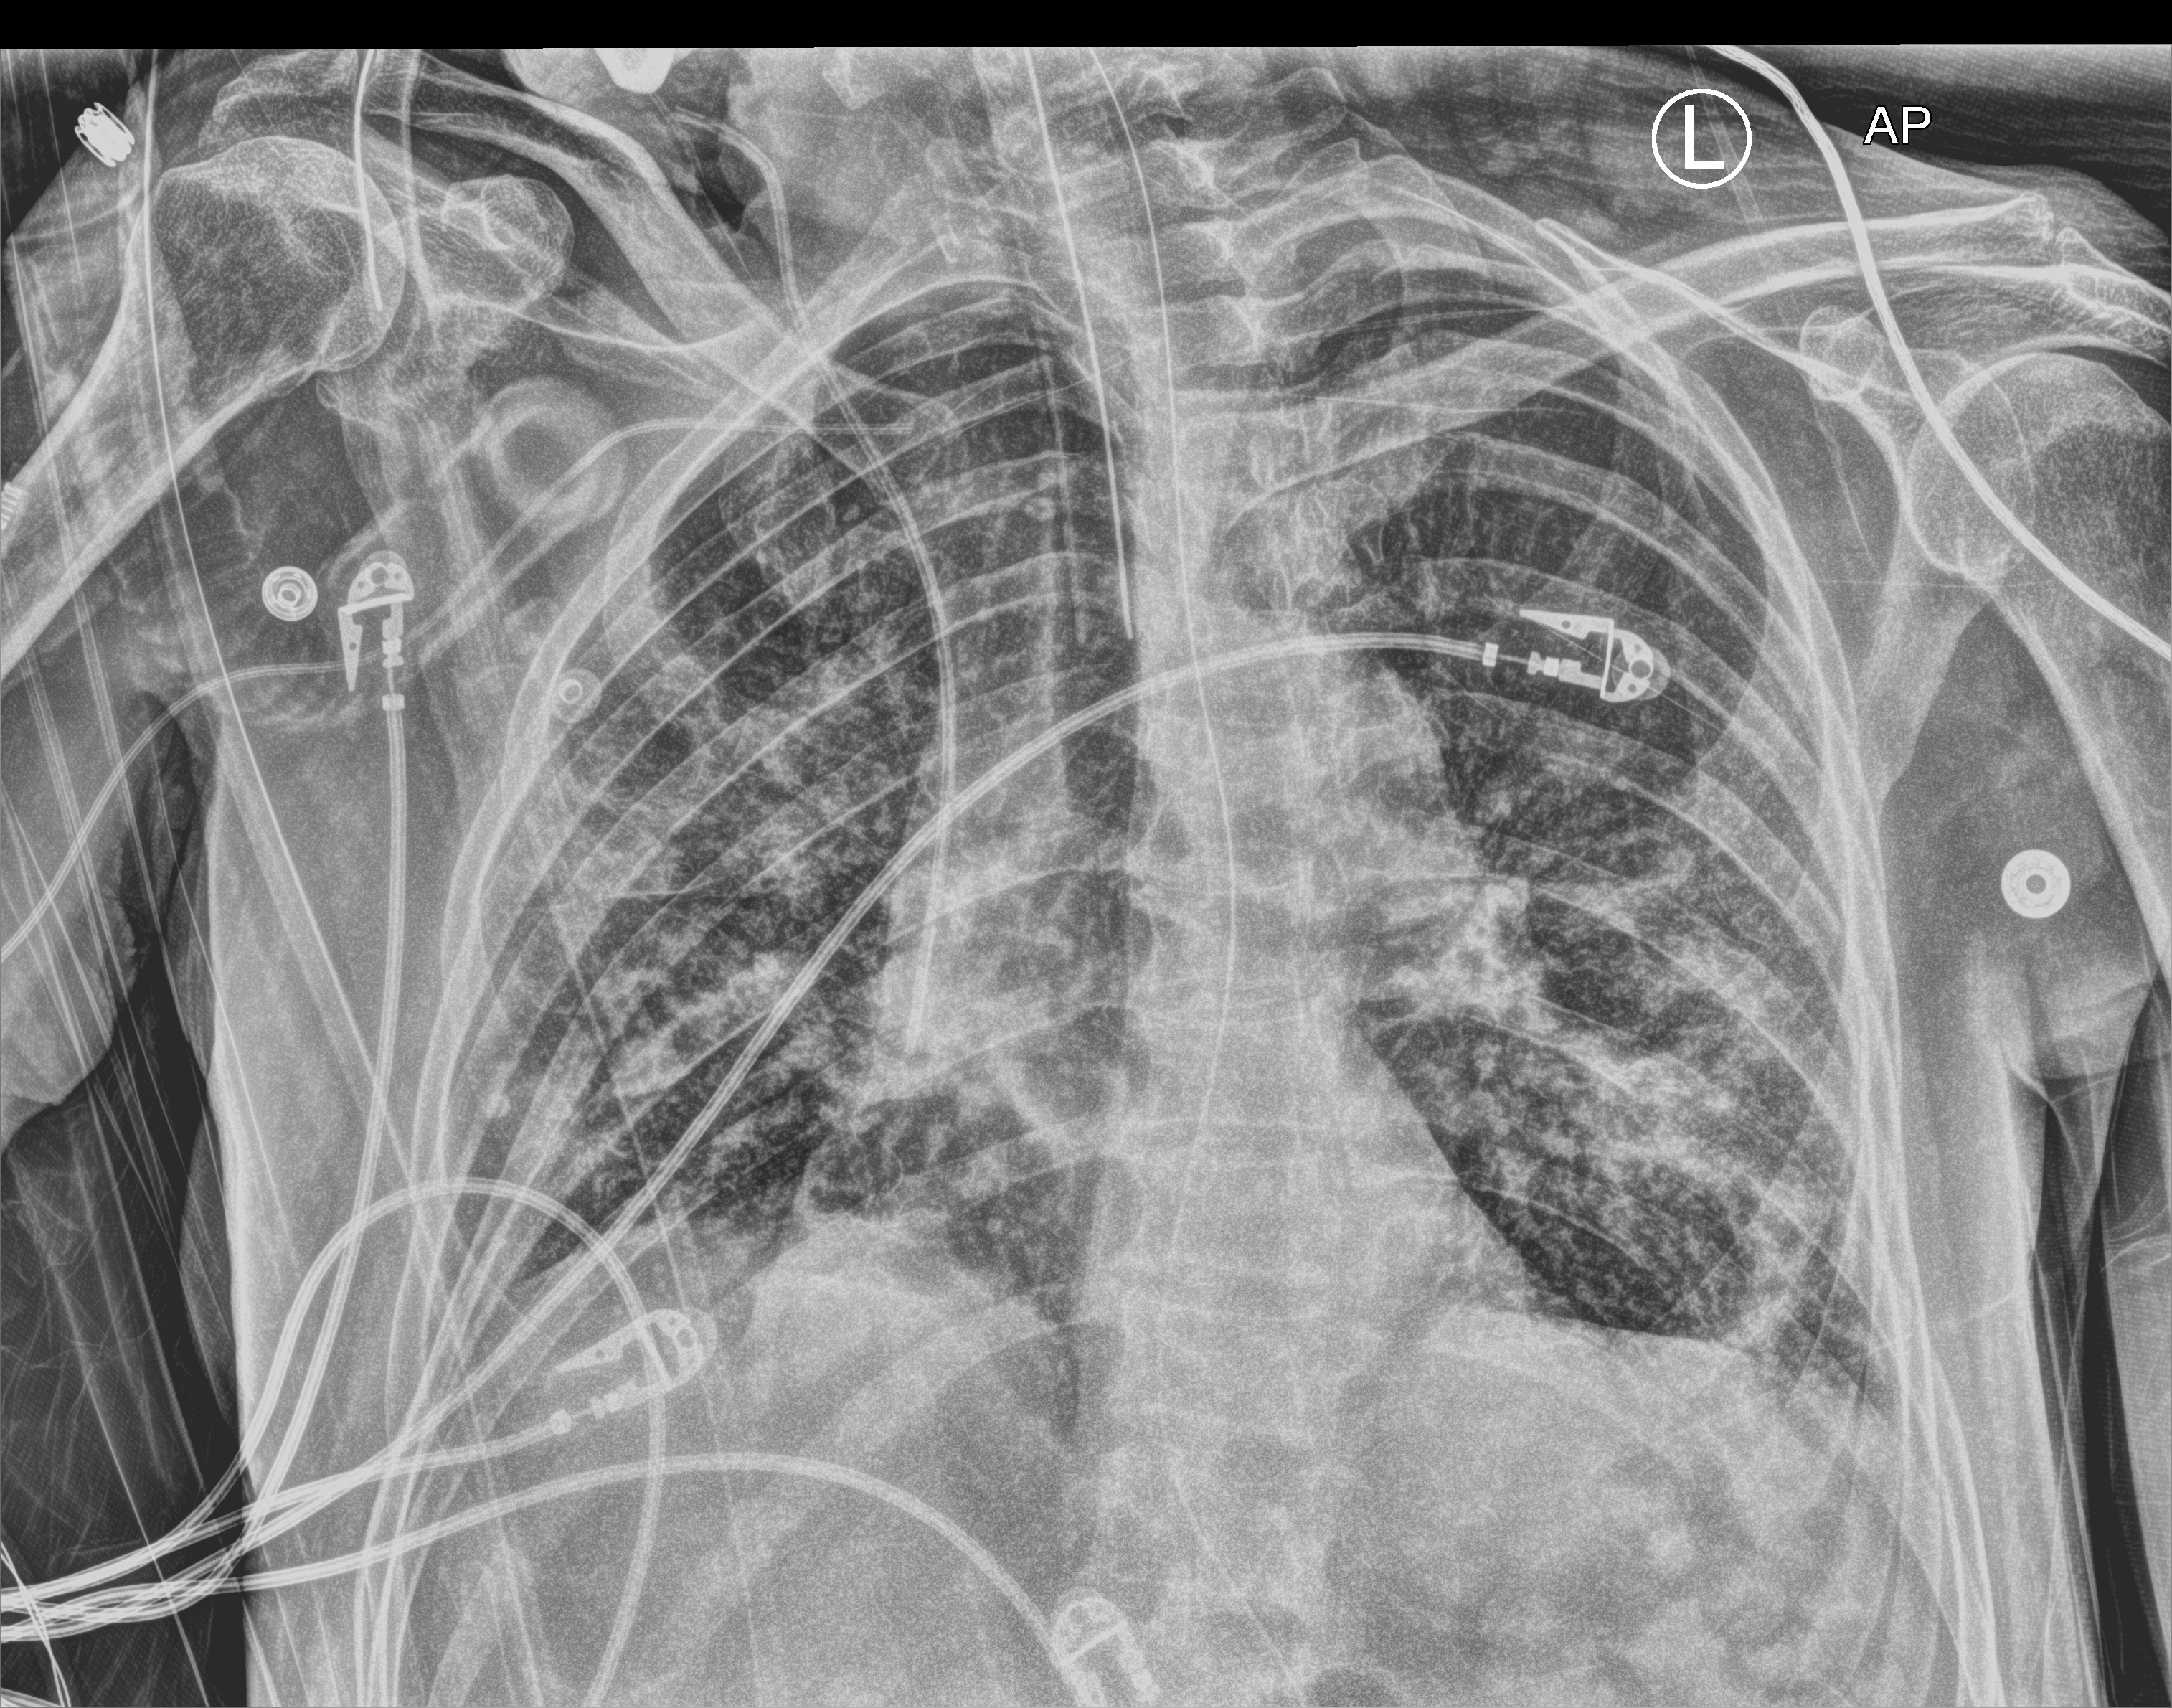
Portable chest radiograph, anteroposterior (AP) projection. Male patient hospitalised with COVID-19, age 75–90 years.
Admission-level facts for this patient (not findings on this image; timing relative to this image not recorded): admitted to intensive care during this hospital stay: yes; mechanically ventilated during this hospital stay: yes; diabetes (admission record): no.